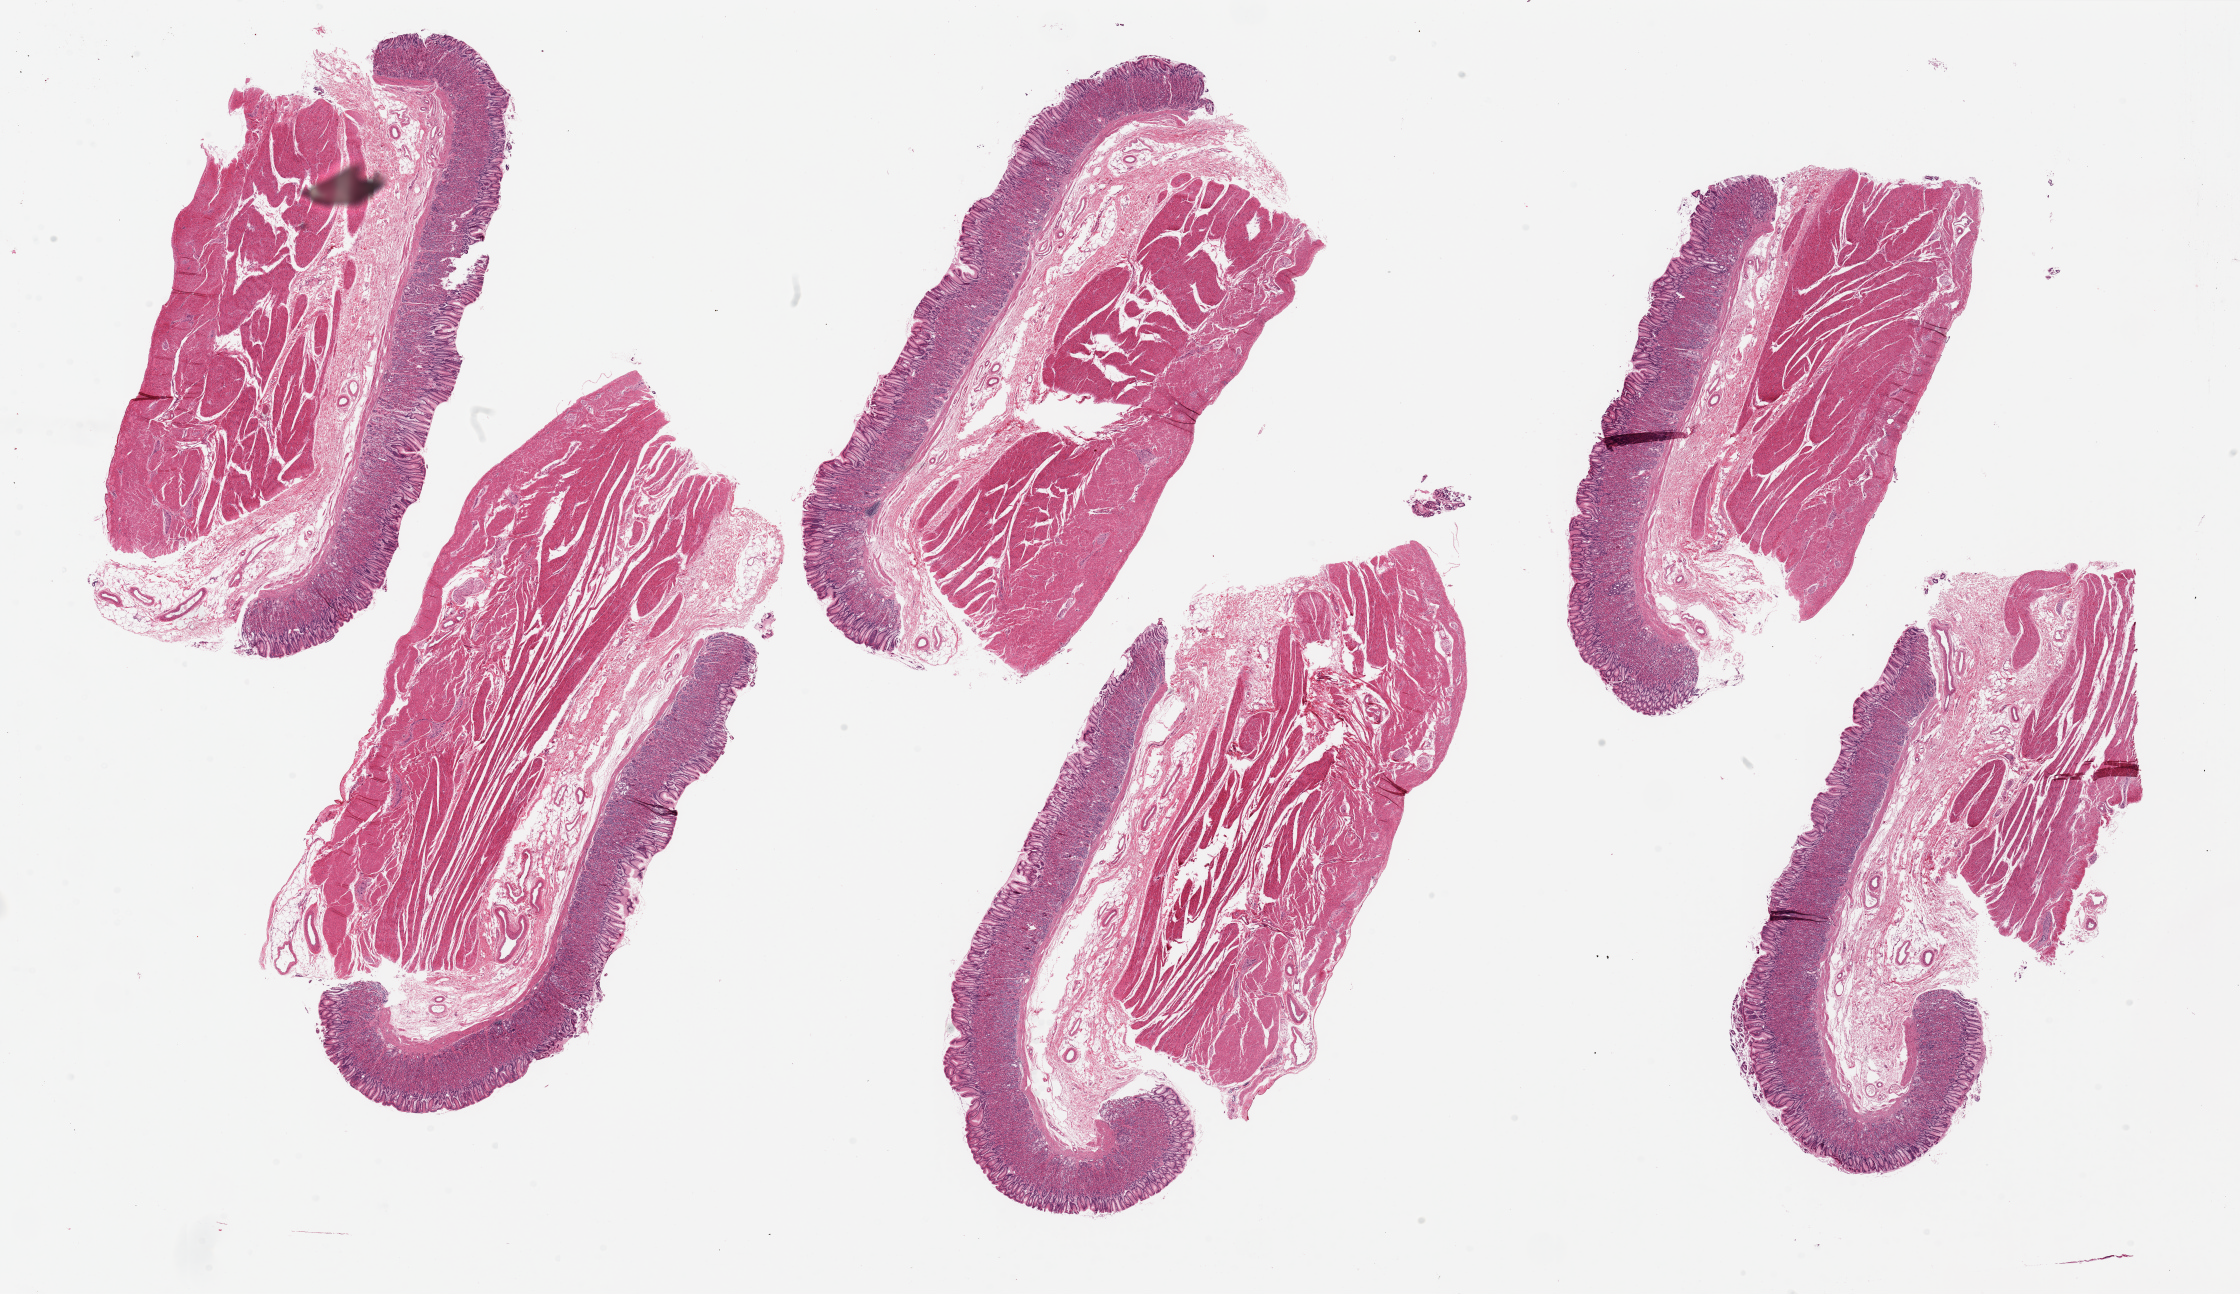
Whole-slide image, H&E stain, whole scanned area (about 35.4 x 20.5 mm) shown as a low-resolution overview, PAXgene-fixed paraffin-embedded (PFPE) section, sampled site (target tissue): stomach, donor tissue sample. Male donor.
Review note (as recorded): 6 pieces, muscoa is ~20-25% of thickness; remarkably well-preserved.